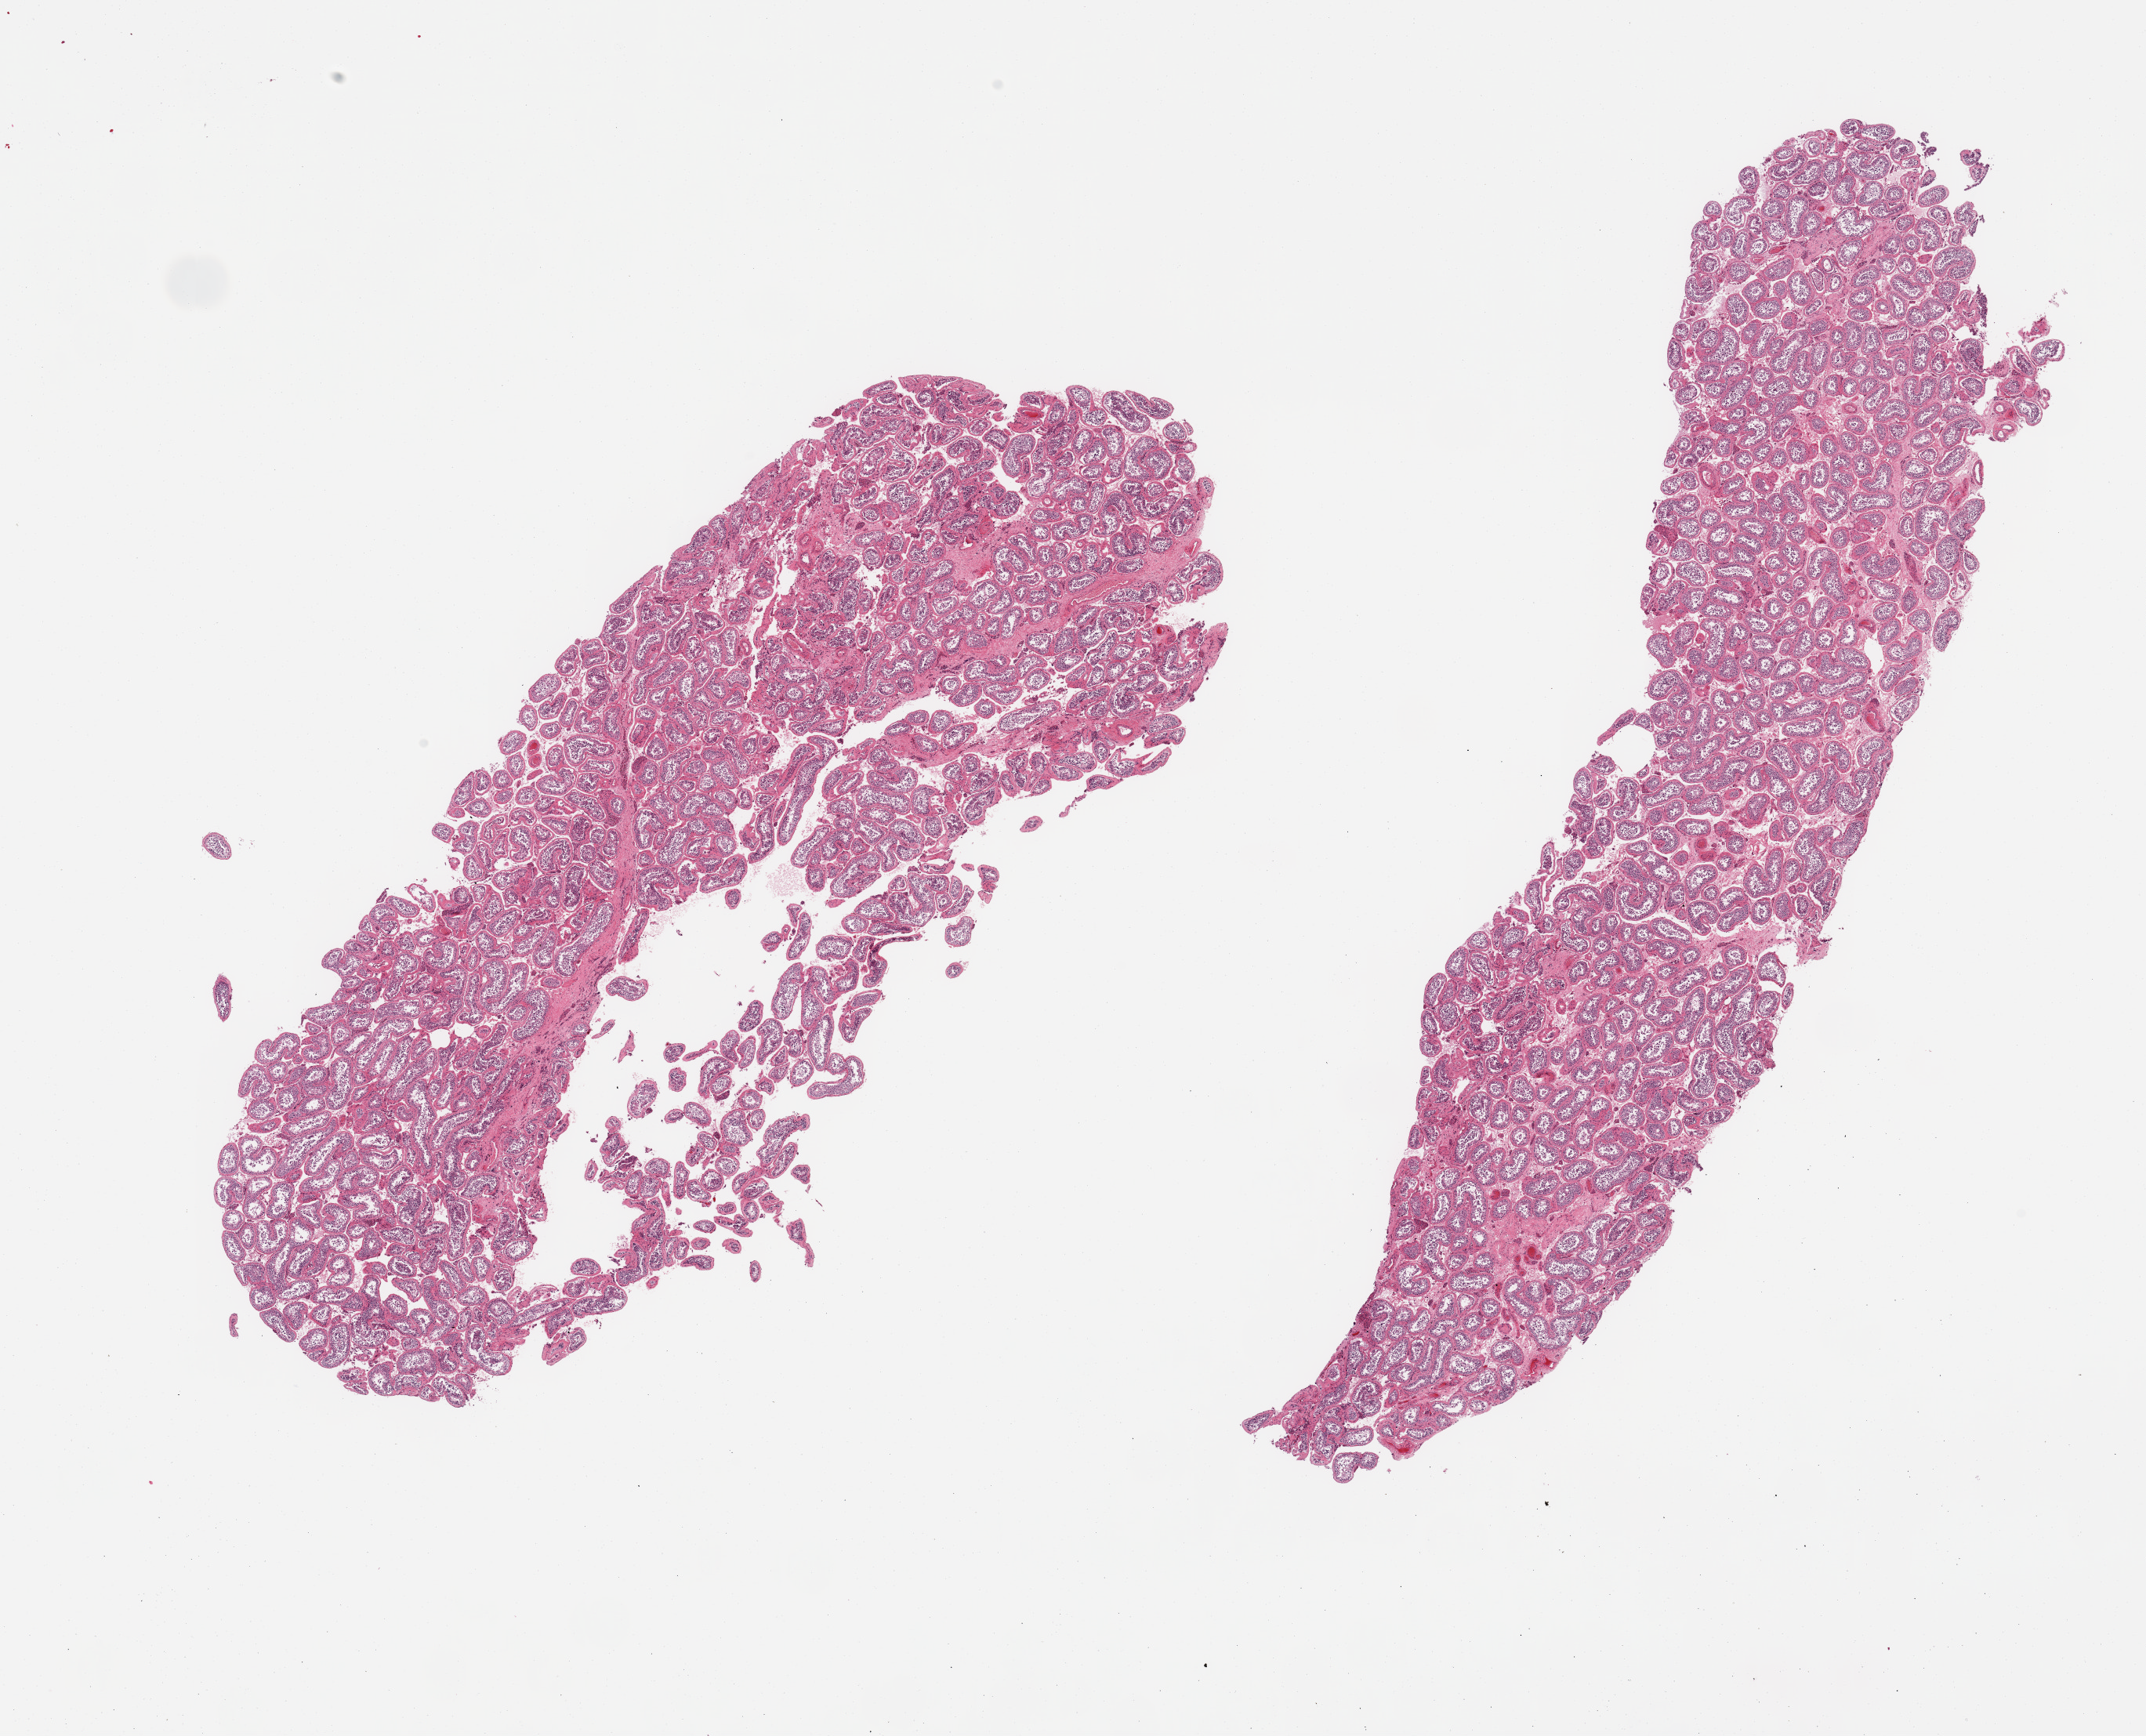
Whole-slide image, H&E stain — whole scanned area (about 21.7 x 17.5 mm) shown as a low-resolution overview, PAXgene-fixed paraffin-embedded (PFPE) section, section of testis (target tissue), tissue donor sample.
- pathologist's review note for this sample: 2 pieces, spermatogenesis present, slightly reduced